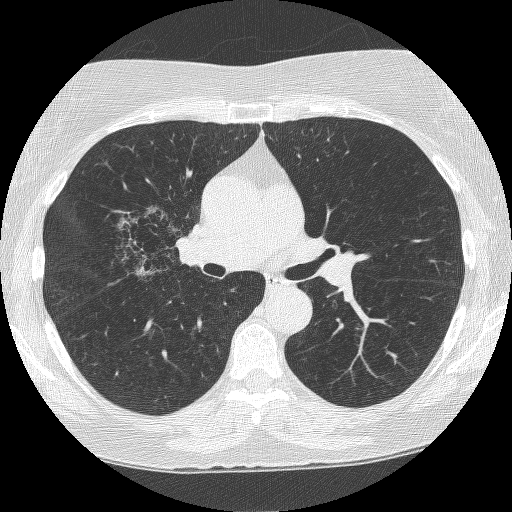
Chest CT (low-dose screening protocol), one axial image; second annual screen; lung window (W 1500 / L -600 HU); 1.25 mm slice thickness. Female, age 64 years at enrolment. Former smoker at enrolment.
- Expert-annotated lung lesion, box from (x=116, y=205) to (x=202, y=287) px.
- The screening reader recorded 4 non-calcified nodules or masses ≥4 mm on this exam; which of them this box marks is not recorded.
- Later outcome: lung cancer diagnosed 381 days after this screen — adenocarcinoma, NOS, right upper lobe, right middle lobe, right hilum, stage IV (AJCC 6th edition), 85 mm at pathology.